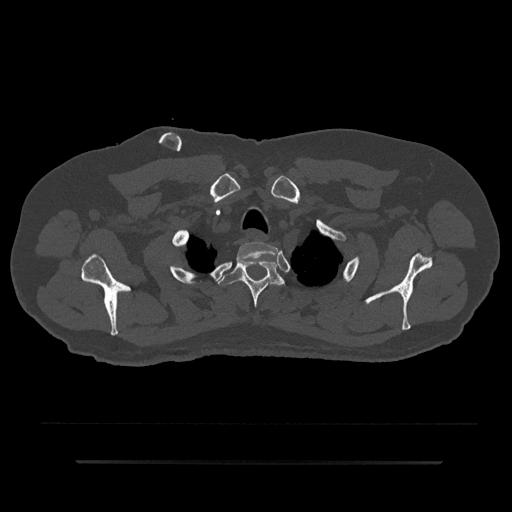
CT including the spine, one axial slice; position 706 of 797 along the scan axis; reconstruction kernel Br40s/3; 120 kVp; bone window (W 1800 / L 400 HU); 0.5 mm slice thickness; 512 × 512 image matrix, field of view 464 × 464 mm. Male patient, age 59 years. Case-level facts recorded for this patient, not image findings: primary cancer: bile ducts; vertebrae with lytic lesions (as recorded): T10.
Annotated regions visible in this slice (semi-automatically segmented with operator editing):
- T1 vertebra: bounding box (x1, y1, x2, y2) in pixels: (236, 242, 278, 263)
- T2 vertebra: (218, 255, 286, 308)